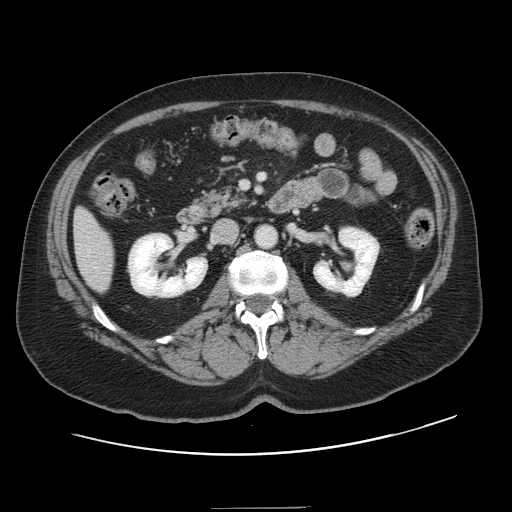
Contrast-enhanced abdominal CT, one axial slice; slice 53 of 143 in the series (ordered by position); intravenous contrast given; soft-tissue window (W 400 / L 40 HU); 2.5 mm slice thickness; 512 × 512 image matrix. Male patient, age 62 years. Case-level facts recorded for this patient, not image findings: diagnosis: colorectal cancer liver metastases, imaged before liver resection; multiple liver metastases: yes; largest metastasis: 2.7 cm; disease in both lobes: no.
Structures marked on this image (outlined manually by an expert reader):
- liver: box from (x=75, y=211) to (x=114, y=291) px